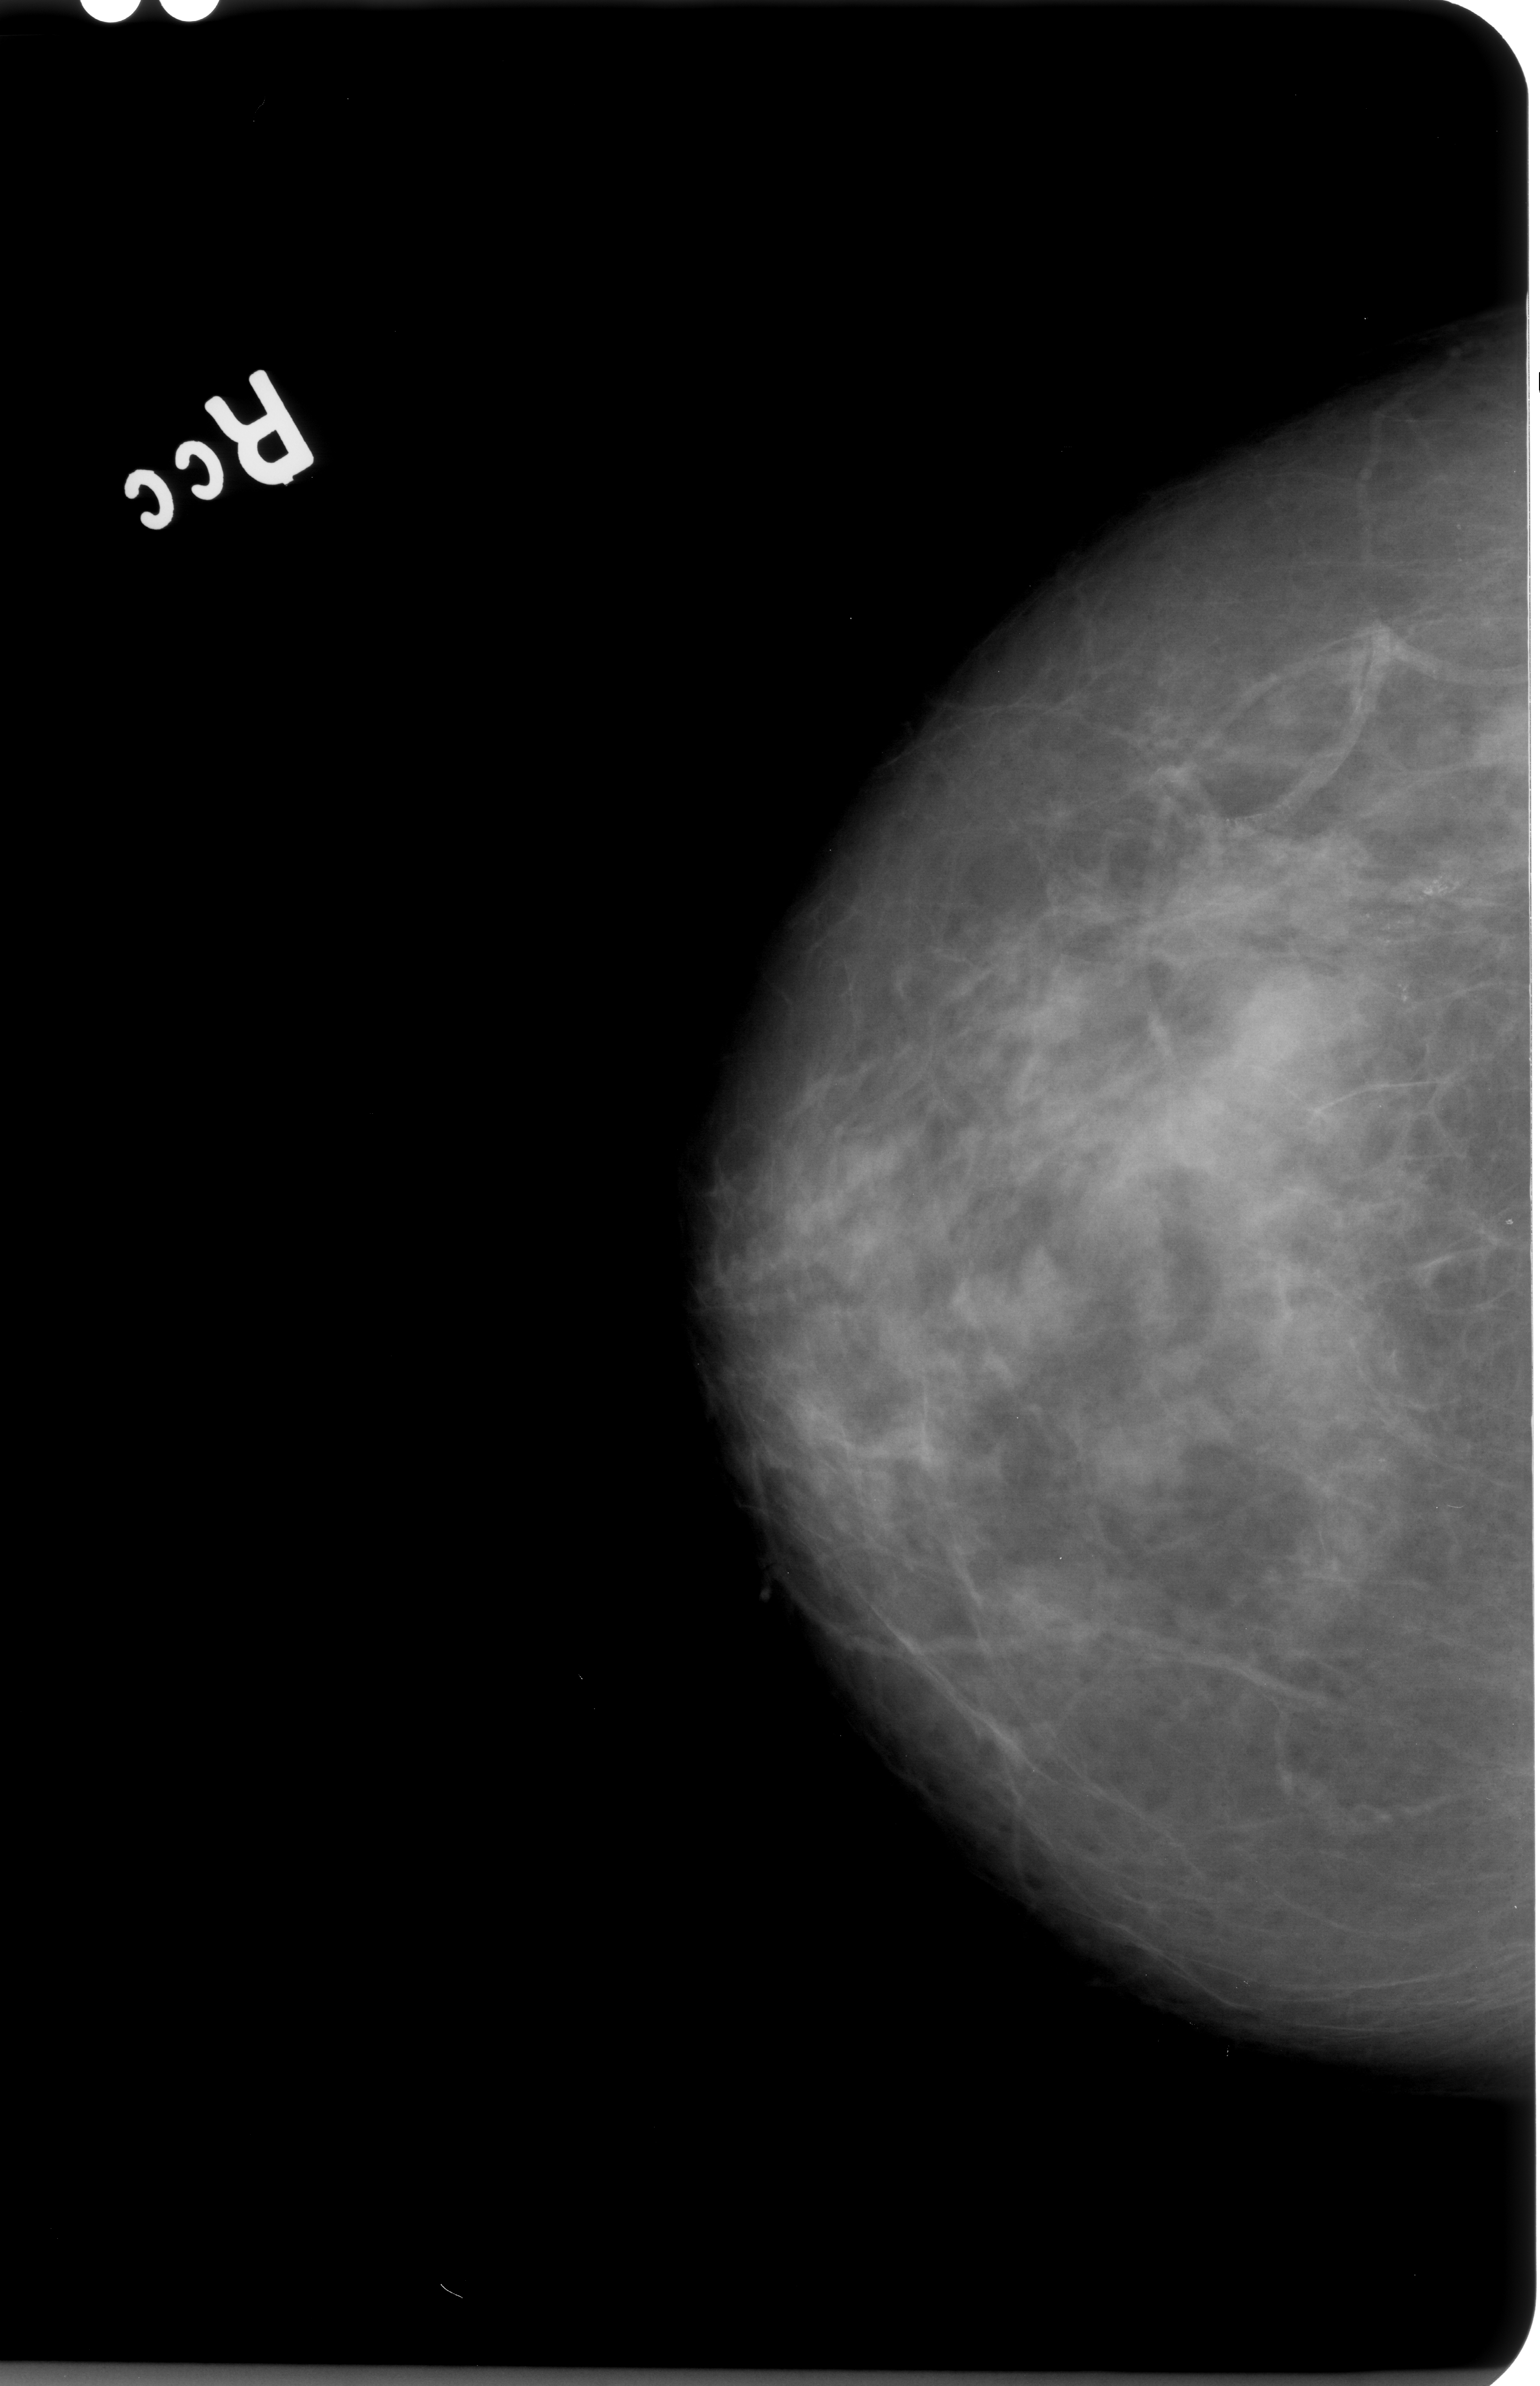
Mammogram (digitized film), right breast, craniocaudal (CC) view, BI-RADS breast density category 3 (scale 1–4).
Marked findings (only marked abnormalities are described; nothing is implied about the rest of the image): calcifications, morphology pleomorphic / fine linear branching, distribution clustered; BI-RADS assessment category 4; pathology result (as recorded, not read from the image): benign.